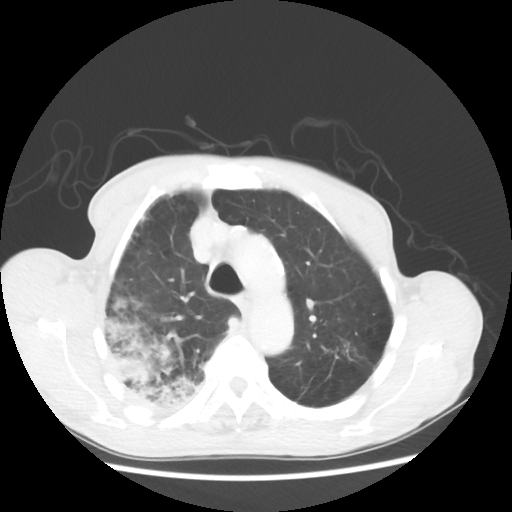
Chest CT, one axial slice. Position 41 of 58 along the scan axis. Reconstruction kernel STANDARD. 100 kVp. Lung window (W 1500 / L -600 HU). 5 mm slice thickness. 512 × 512 image matrix, field of view 351 × 351 mm. Male patient, age 75 years. From the clinical record (not read from this slice): clinical TNM (as recorded): T4 N1 M1.
Structures marked on this image (rectangle marked by the reading radiologist):
- lung tumour (recorded histology: adenocarcinoma): bounding box (x1, y1, x2, y2) in pixels: (103, 295, 202, 404)